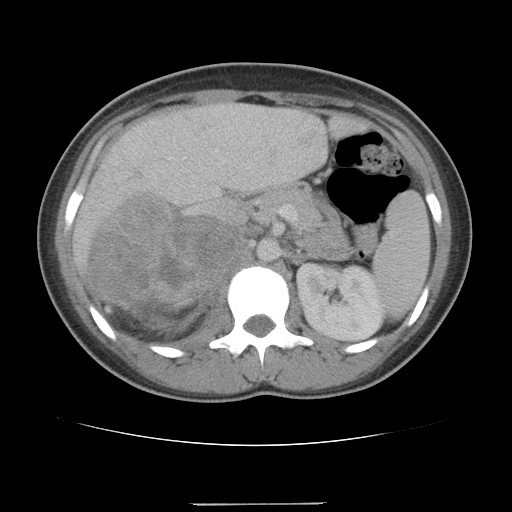
Contrast-enhanced abdominal CT, one axial slice. Slice 68 of 100 in the series (ordered by position). Reconstruction kernel STANDARD. 120 kVp. Intravenous contrast given. Soft-tissue window (W 400 / L 40 HU). 5 mm slice thickness. 512 × 512 image matrix, field of view 360 × 360 mm. Female patient, age 21 years. From the clinical record (not read from this slice): diagnosis: adrenocortical carcinoma; tumour side: right adrenal; tumour size at pathology: 15.5 cm; Ki-67 index: 26 %; stage (as recorded): 3.
Structures marked on this image (semi-automatically segmented with operator editing):
- mass: box from (x=90, y=193) to (x=235, y=332) px